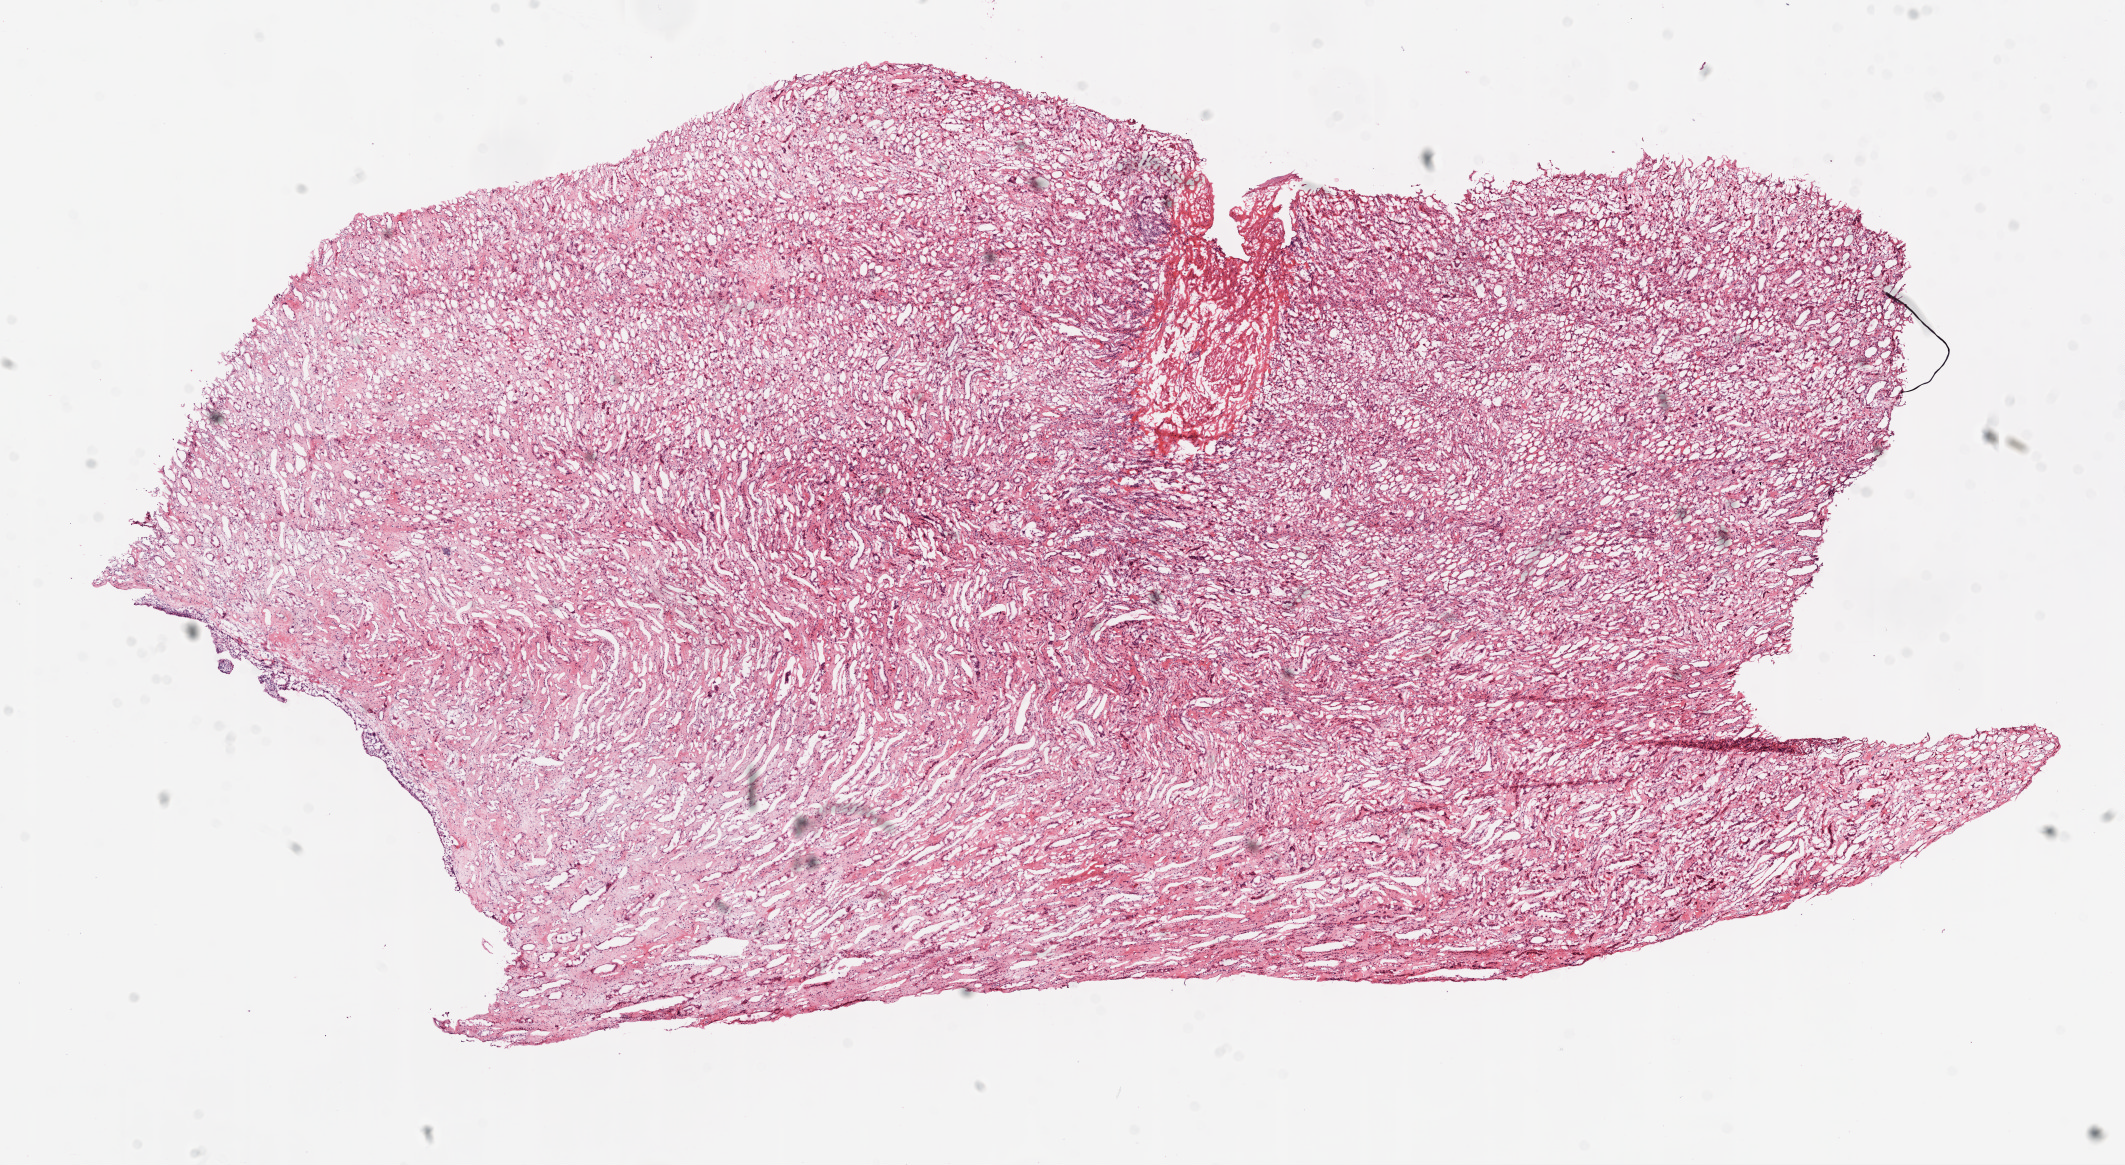
Whole-slide histology image, H&E — whole scanned area (about 17.1 x 9.3 mm) shown as a low-resolution overview. Frozen section. Sample: solid tissue normal (non-tumour tissue), kidney. Female, age 79 years at initial diagnosis.
This section: solid tissue normal sample (biorepository sample class). Patient diagnosis: Clear cell adenocarcinoma, NOS.